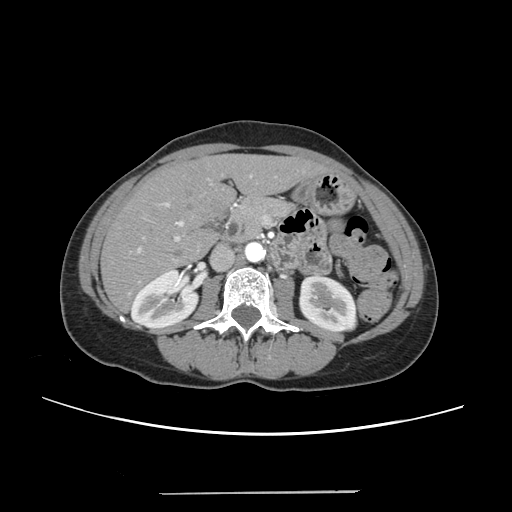
Contrast-enhanced abdominal CT, one axial slice; 120 kVp; intravenous contrast given; soft-tissue window (W 400 / L 40 HU); 512 × 512 image matrix, field of view 371 × 371 mm. Female patient, age 60 years. From the clinical record (not read from this slice): diagnosis: colorectal cancer liver metastases, imaged before liver resection; multiple liver metastases: no; largest metastasis: 1.5 cm; disease in both lobes: no.
Structures marked on this image (outlined manually by an expert reader):
- liver: bounding box (x1, y1, x2, y2) in pixels: (103, 156, 322, 309)
- planned liver remnant (the part of the liver to remain after resection): (103, 157, 322, 309)
- portal vein (with intrahepatic branches): (136, 175, 252, 252)